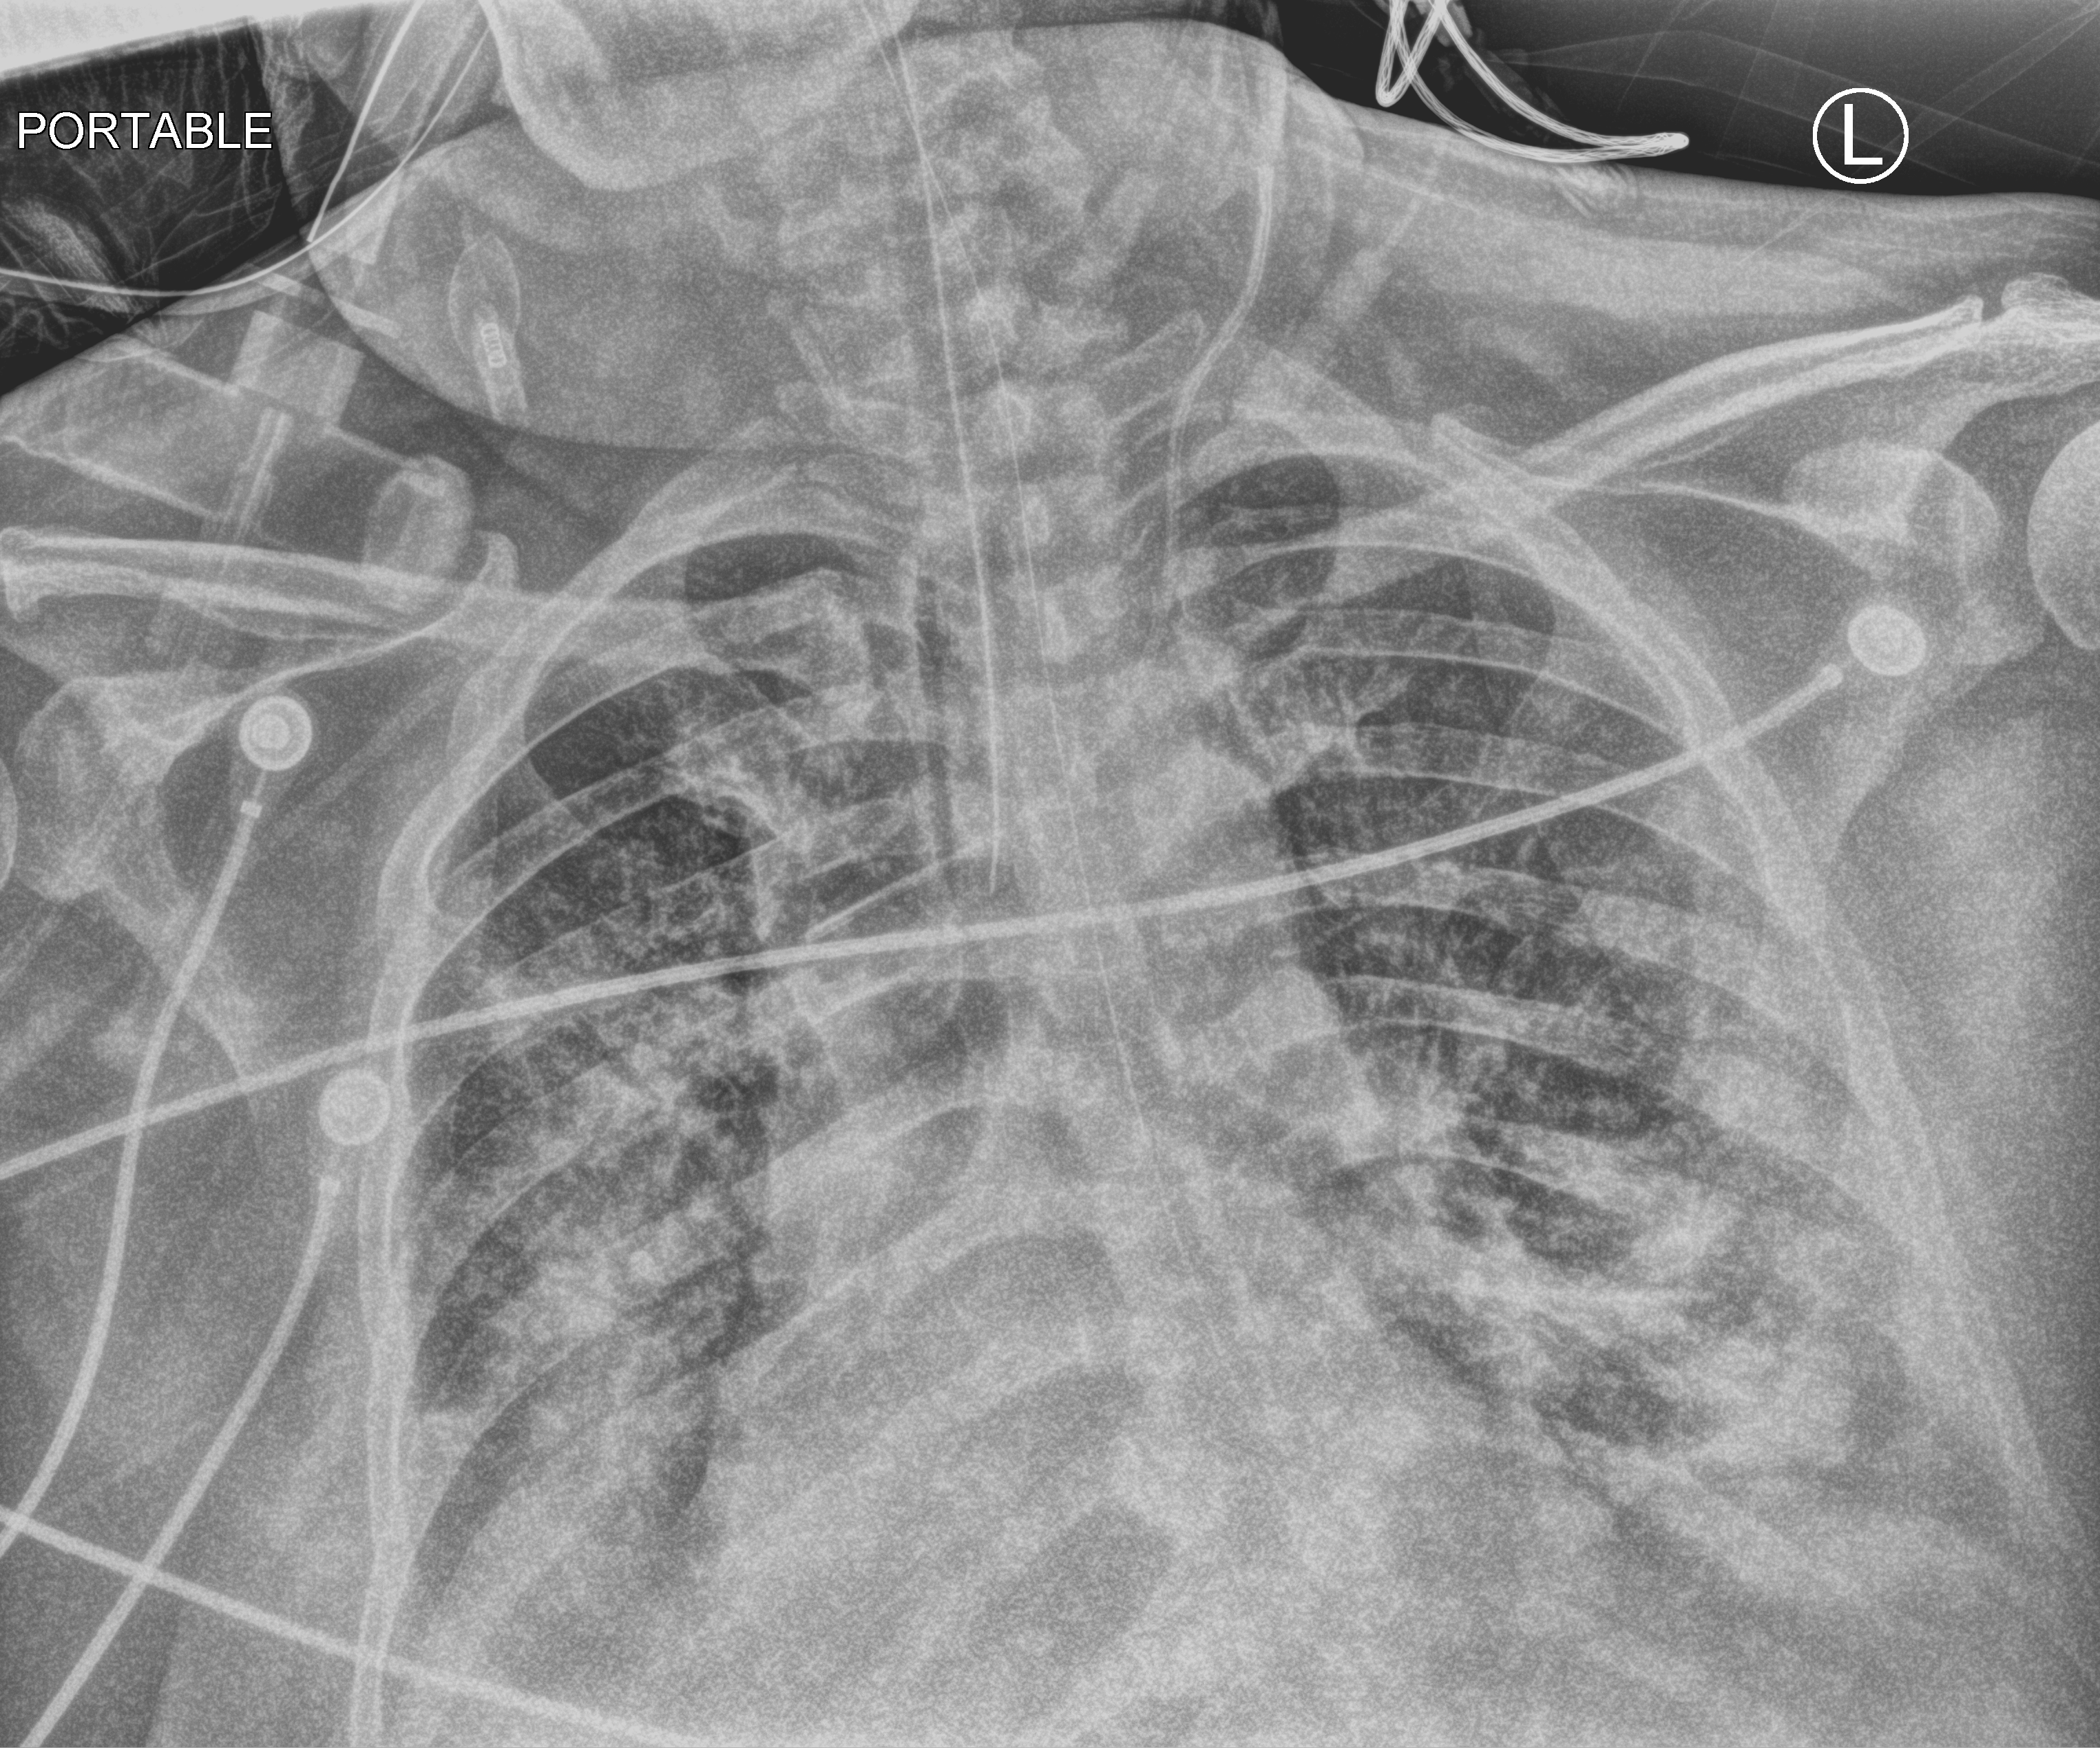
Chest X-ray (portable); anteroposterior (AP) projection. Adult patient hospitalised with COVID-19, age 18–59 years.
Admission-level facts for this patient (not findings on this image; timing relative to this image not recorded): smoking status (admission record): never; admitted to intensive care during this hospital stay: yes.